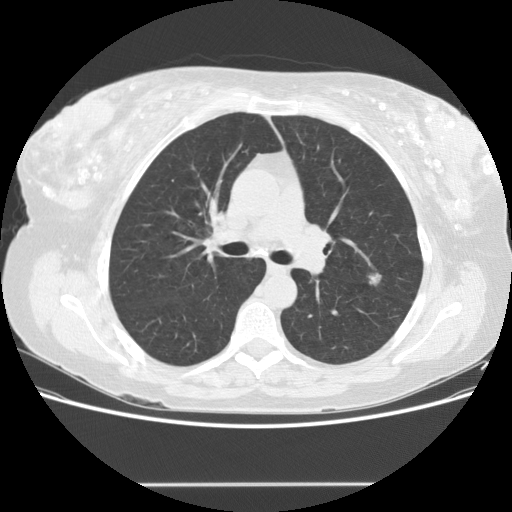
Low-dose screening chest CT, axial slice, second annual screen, lung window (W 1500 / L -600 HU), 2.5 mm slice thickness, standard (soft-tissue) reconstruction kernel (STANDARD), 120 kVp, slice 56 of 151 in the series, 512 × 512 image matrix, field of view 360 × 360 mm. Female, age 57 years at enrolment. Current smoker at enrolment.
Expert reader's lesion annotation, box from (x=357, y=266) to (x=389, y=293) px. Screening reader's record for this exam (one nodule recorded; not confirmed to be the boxed lesion): non-calcified nodule or mass ≥4 mm, lingula, 10 × 8 mm, smooth margins, soft tissue attenuation, pre-existing on the prior screen: no.